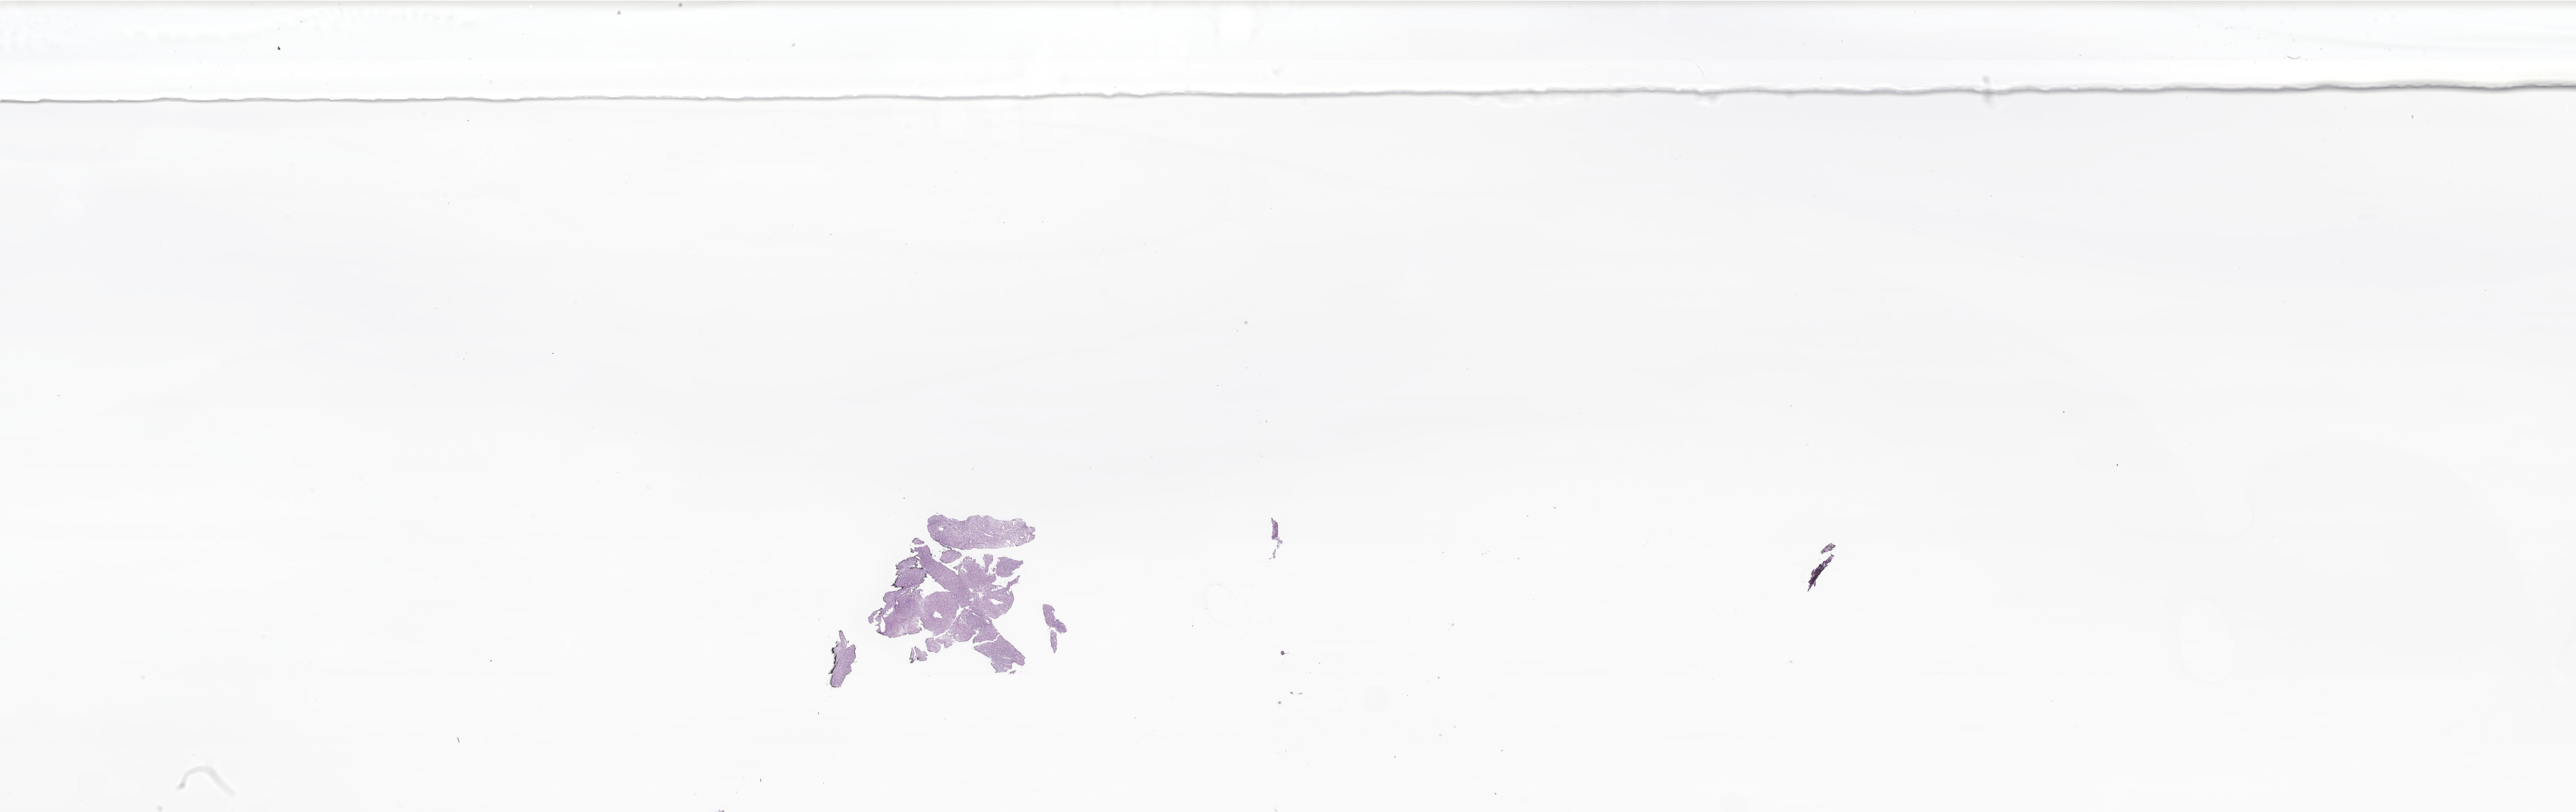
Digitized hematoxylin and eosin (H&E)-stained section of tumor tissue from the soft tissue of upper extremity, shown as a low-resolution overview of the whole scanned area (about 40.2 x 12.7 mm). Formalin-fixed, paraffin-embedded (FFPE) tissue. Male patient, age 129 days.
Diagnosis: Infantile fibrosarcoma. Tissue or organ of origin (case record): connective, subcutaneous and other soft tissues of upper limb and shoulder.